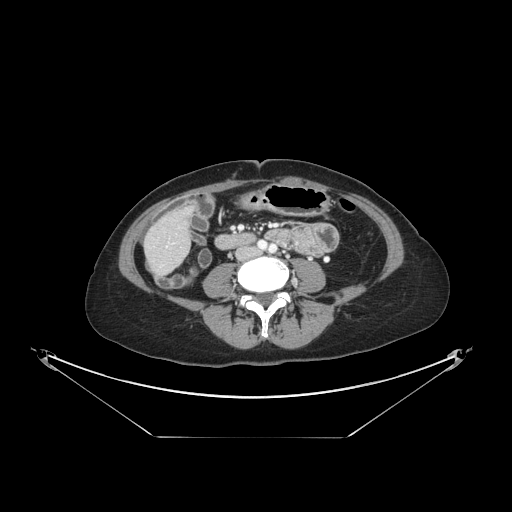
Contrast-enhanced abdominal CT, one axial slice. Slice 28 of 148 in the series (ordered by position). Reconstruction kernel STANDARD. 120 kVp. Intravenous contrast given. Soft-tissue window (W 400 / L 40 HU). 2.5 mm slice thickness. 512 × 512 image matrix, field of view 500 × 500 mm. Female patient, age 73 years. Case-level facts recorded for this patient, not image findings: diagnosis: colorectal cancer liver metastases, imaged before liver resection.
Annotated regions visible in this slice (expert manual segmentation):
- liver: bounding box [x1, y1, x2, y2] px = [147, 210, 190, 273]
- planned liver remnant (the part of the liver to remain after resection): [165, 210, 188, 235]